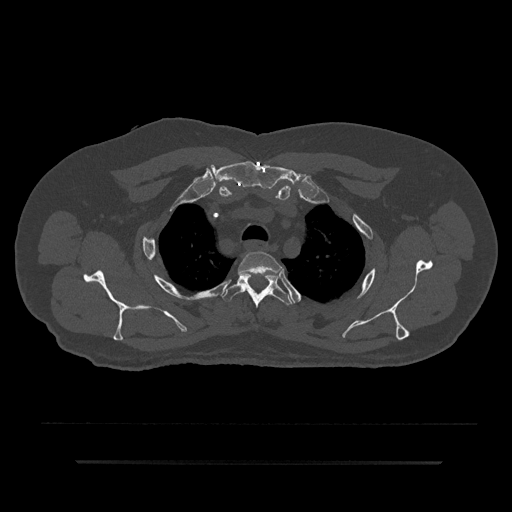
CT including the spine, one axial slice. Slice 672 of 797 in the series (ordered by position). Reconstruction kernel Br40s/3. 120 kVp. Bone window (W 1800 / L 400 HU). 0.5 mm slice thickness. 512 × 512 image matrix. Male patient, age 59 years. From the clinical record (not read from this slice): primary cancer: bile ducts; vertebrae with lytic lesions (as recorded): T10.
Annotated regions visible in this slice (semi-automatic segmentation, software-assisted and operator-edited):
- T2 vertebra: bounding box <238,252,282,275> (left, top, right, bottom; pixels)
- T3 vertebra: <223,273,293,308>